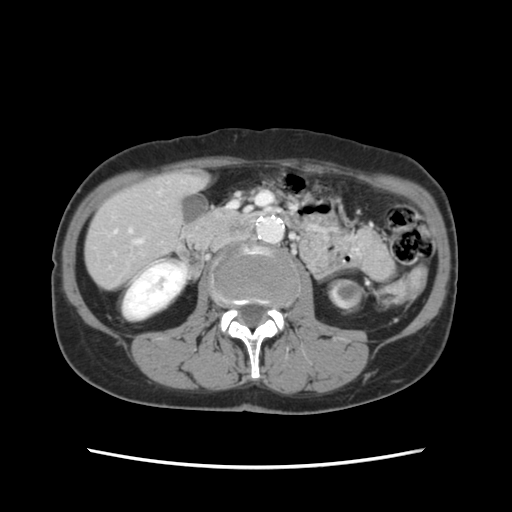
Contrast-enhanced abdominal CT, one axial slice; intravenous contrast given; soft-tissue window (W 400 / L 40 HU); 512 × 512 image matrix. Female patient, age 70 years. From the clinical record (not read from this slice): diagnosis: colorectal cancer liver metastases, imaged before liver resection; multiple liver metastases: no.
Annotated regions visible in this slice (expert manual segmentation):
- hepatic veins: box from (x=135, y=240) to (x=140, y=243) px
- liver: (x=86, y=174)–(x=203, y=288)
- planned liver remnant (the part of the liver to remain after resection): (x=86, y=173)–(x=203, y=289)
- portal vein (with intrahepatic branches): (x=129, y=230)–(x=132, y=233)